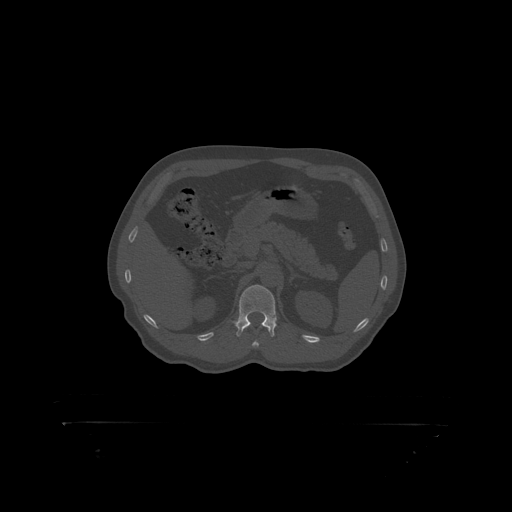
CT including the spine, one axial slice. Position 332 of 399 along the scan axis. Reconstruction kernel STANDARD. Bone window (W 1800 / L 400 HU). 1.25 mm slice thickness. 512 × 512 image matrix, field of view 650 × 650 mm. Male patient, age 46 years. Case-level facts recorded for this patient, not image findings: primary cancer: skin.
Outlined on this slice (semi-automatically segmented with operator editing):
- L1 vertebra: bounding box <239,285,276,319> (left, top, right, bottom; pixels)